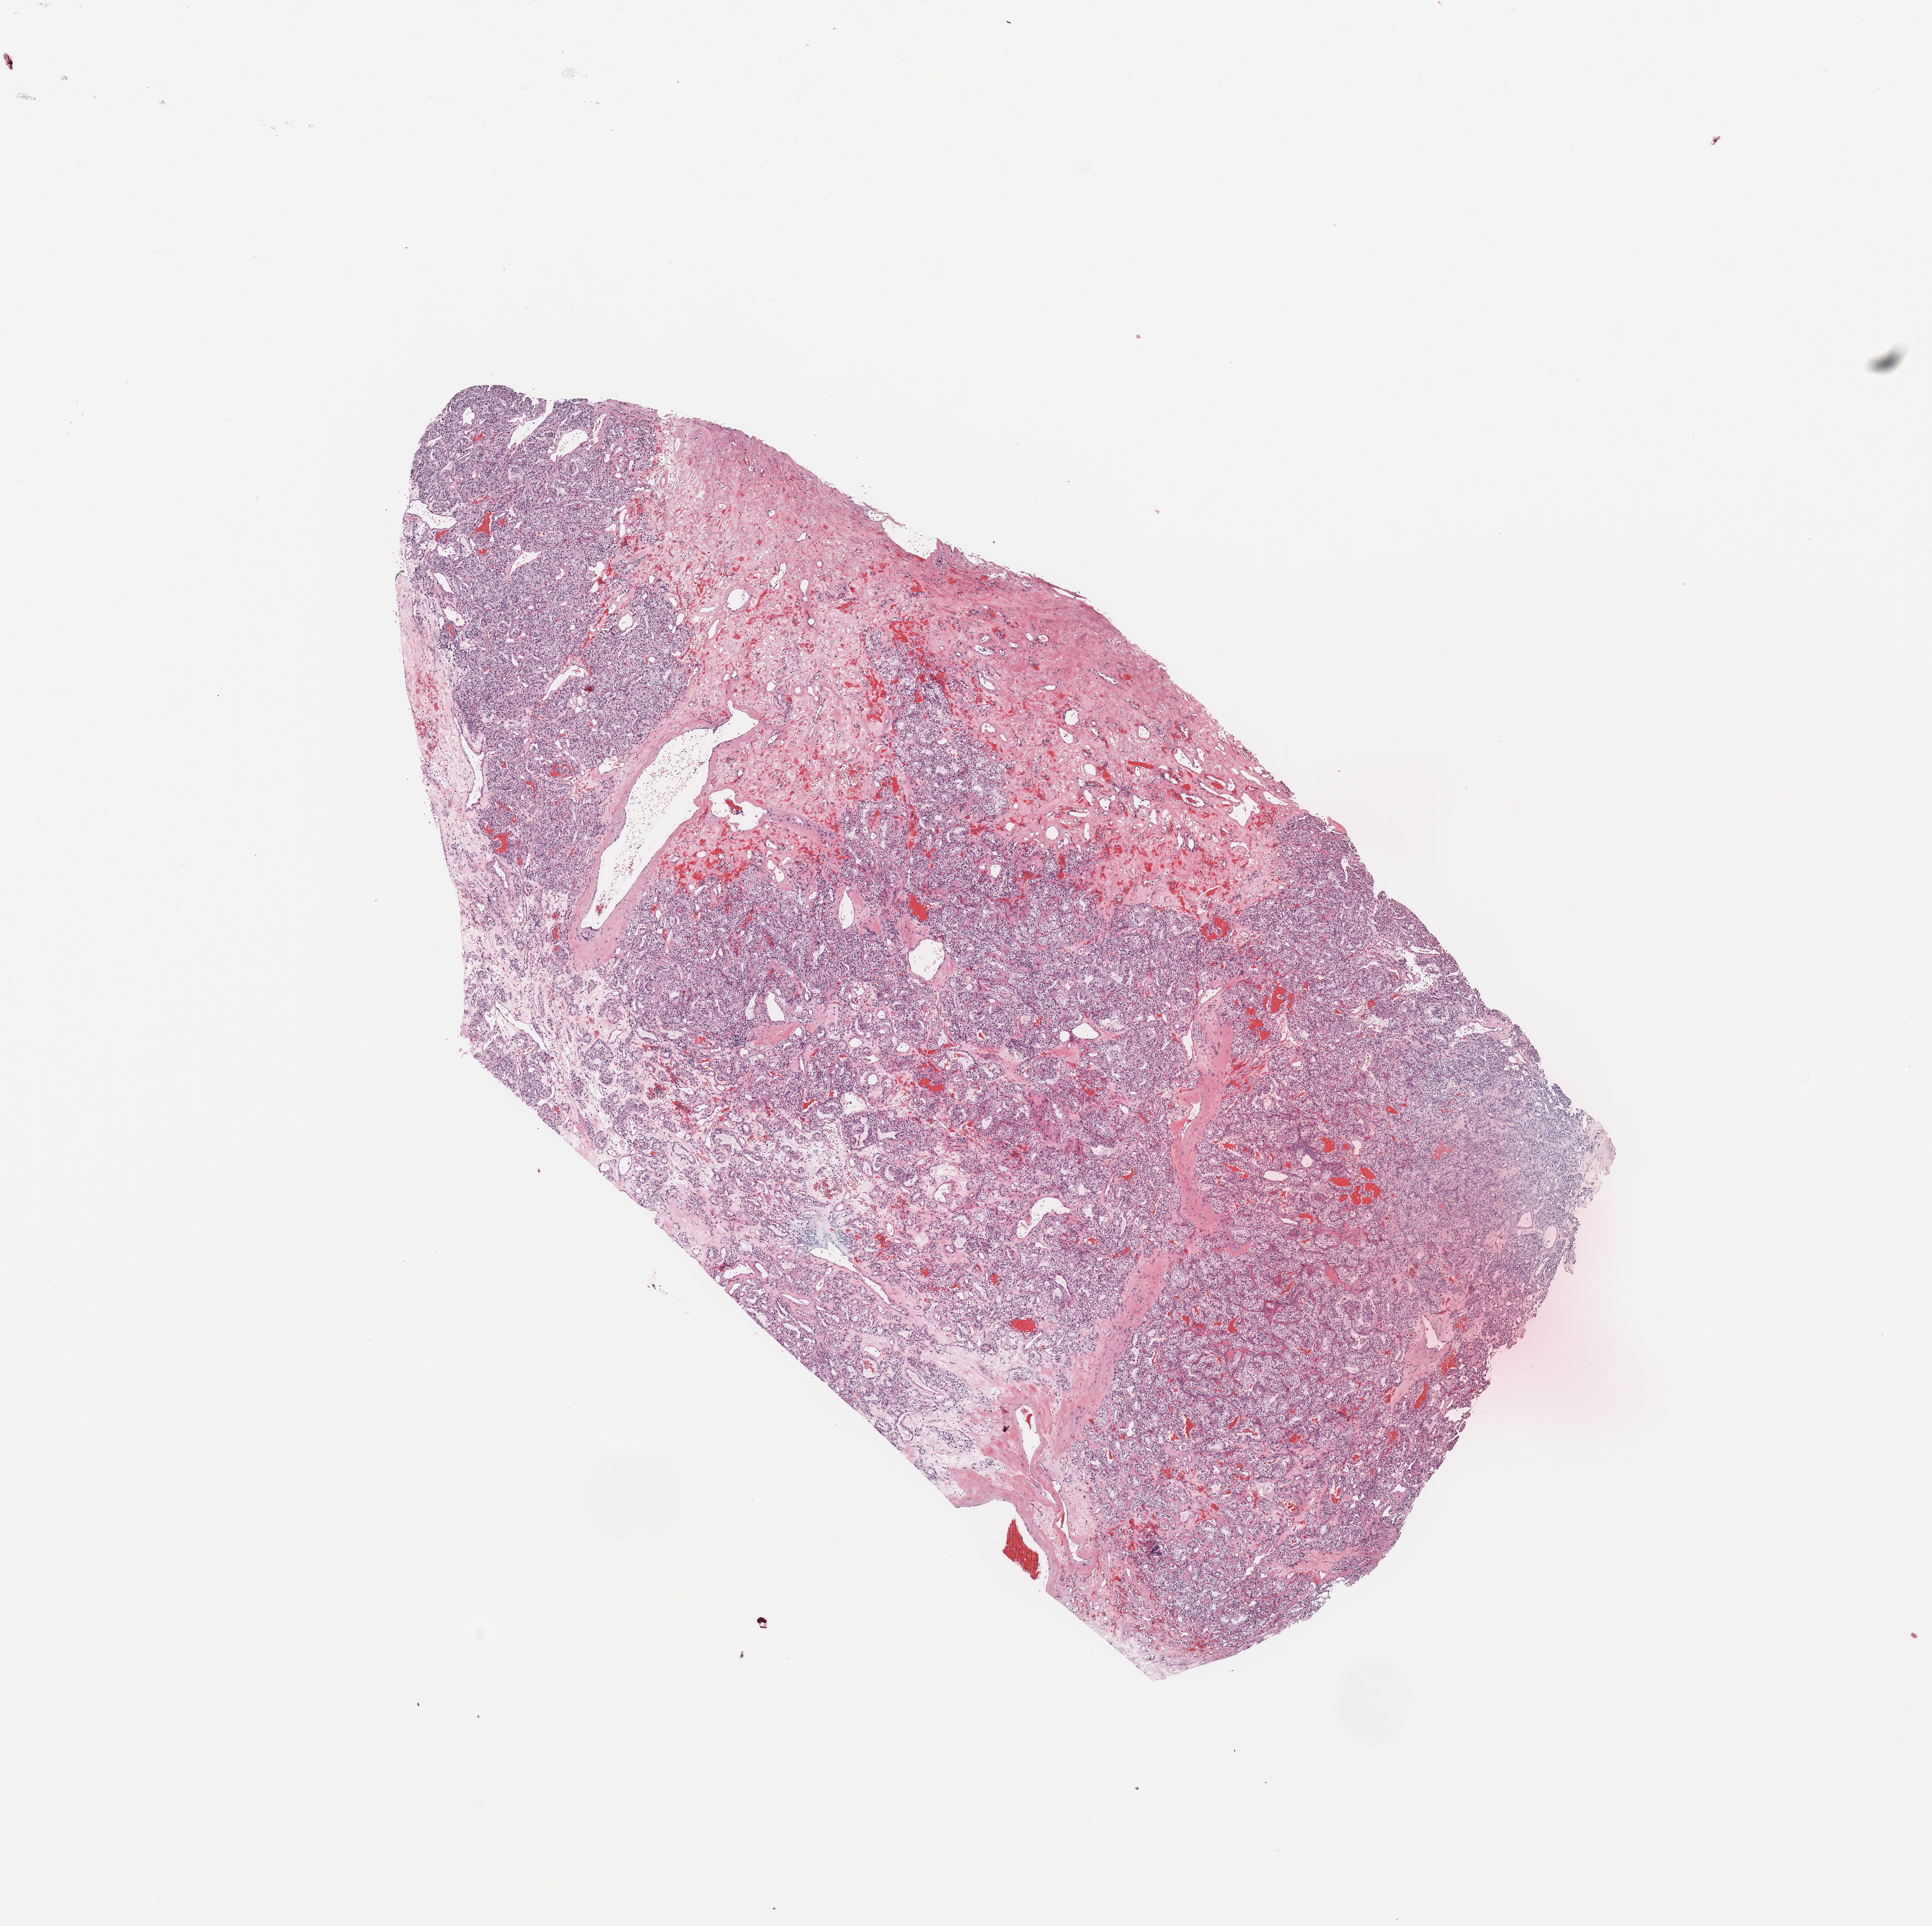
H&E-stained whole-slide image — a low-resolution overview of the entire scanned area, about 11.8 x 11.8 mm (acquisition: 20x scan); tumour tissue sample, sampled site: kidney. Patient: male, age 50 years.
Diagnosis: Renal cell carcinoma, NOS.